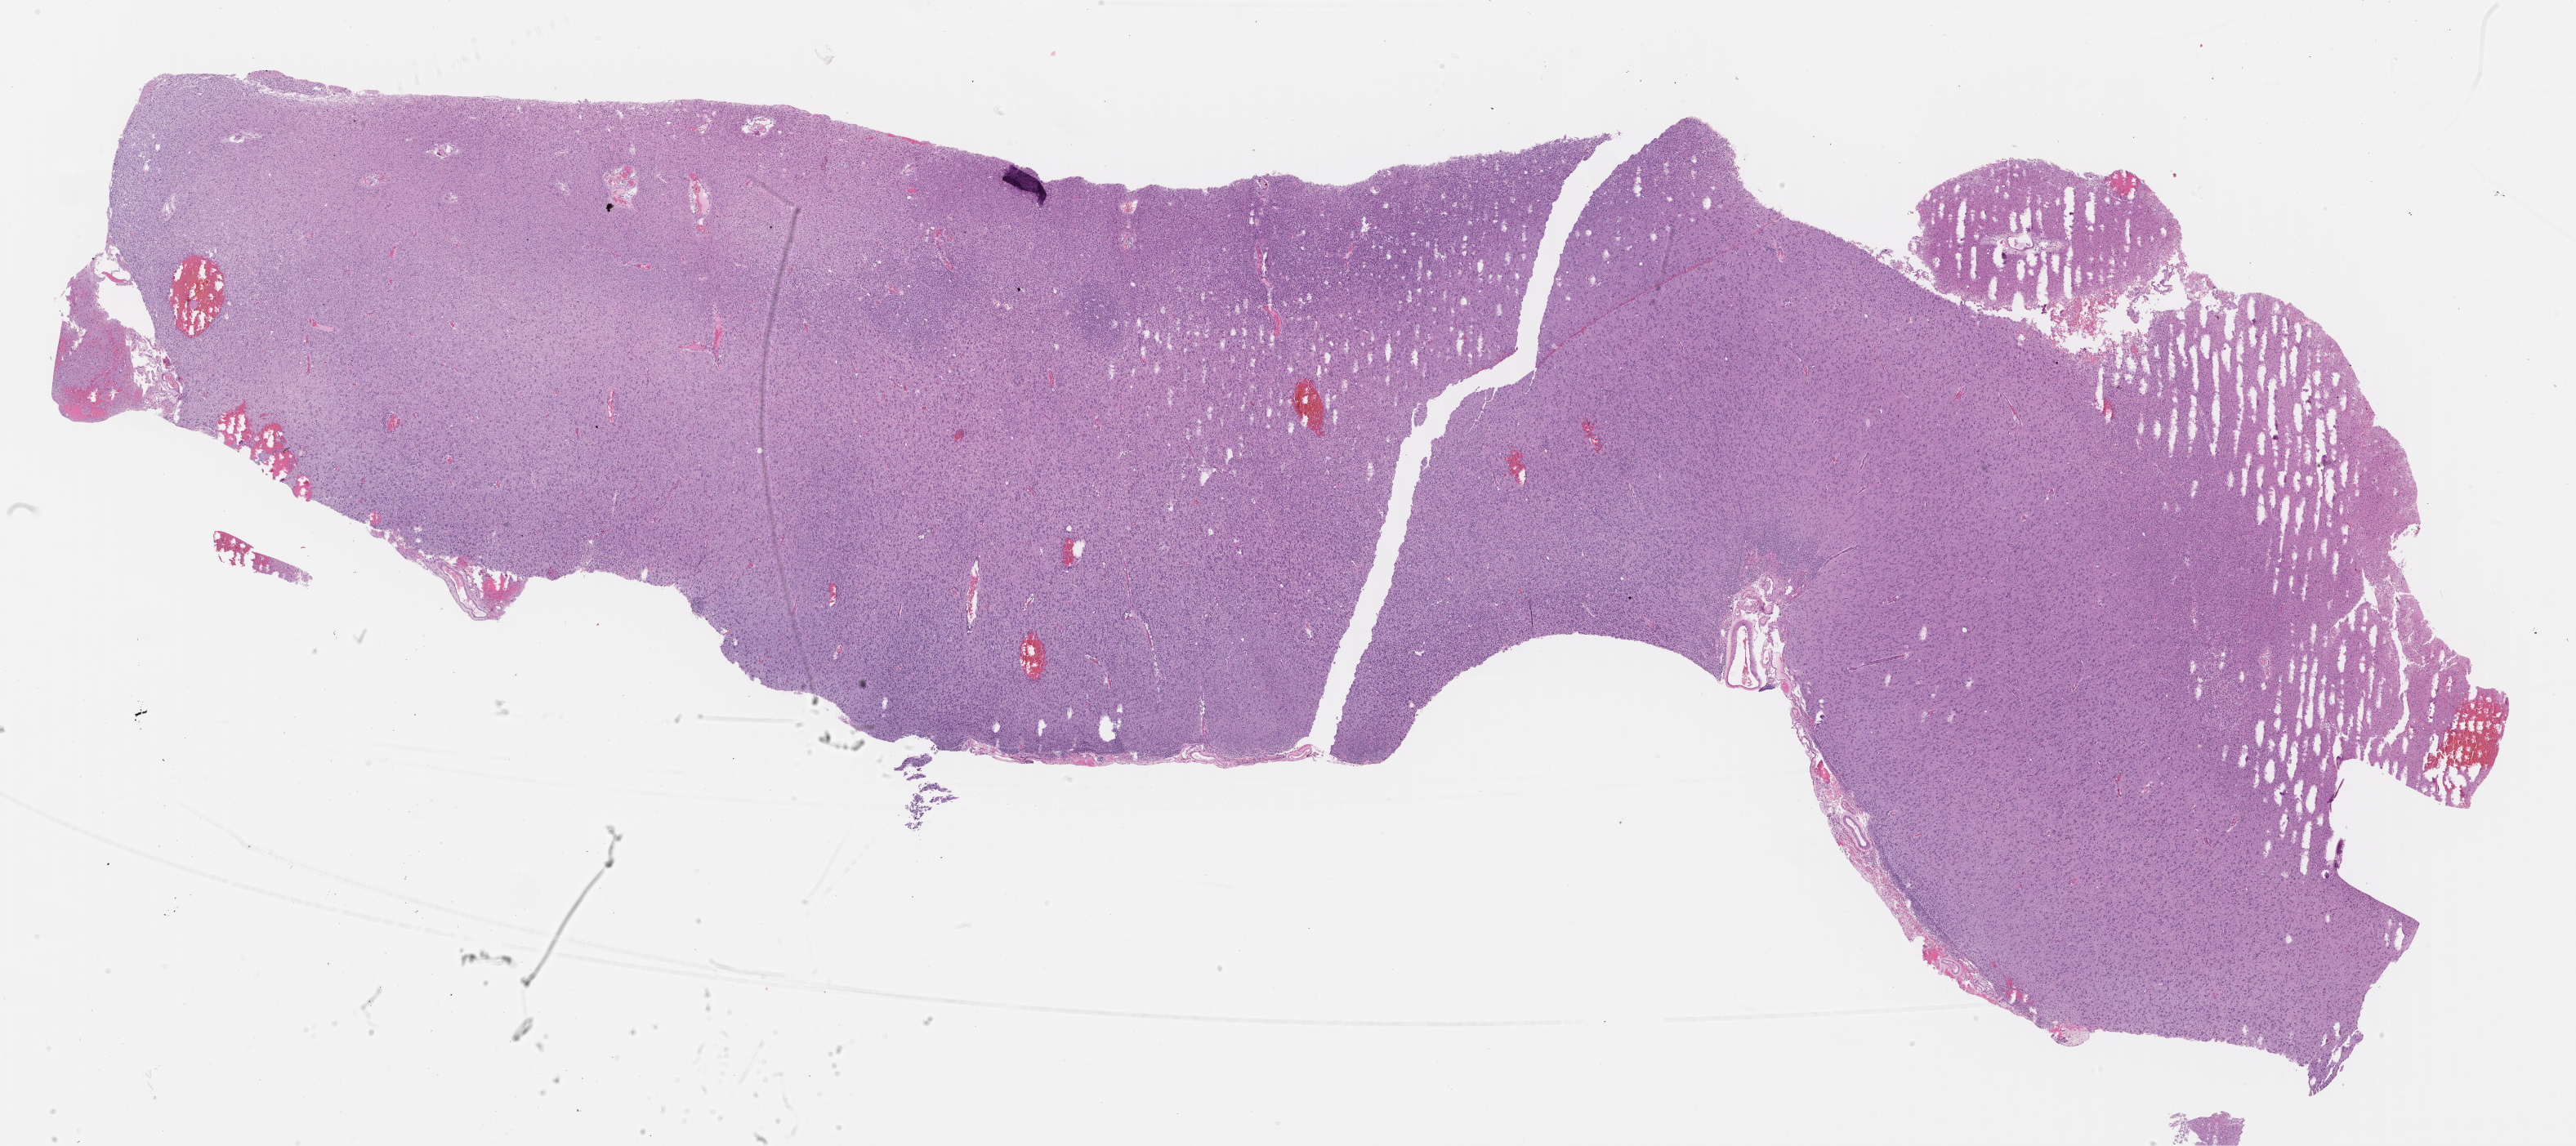
H&E whole-slide image — shown as a low-resolution overview of the whole scanned area (about 25.4 x 11.3 mm); FFPE section; sample: primary tumour, brain. Female, age 53 years at initial diagnosis. Histologic grade: G2 (moderately differentiated).
- laterality: right
- diagnosis: Oligodendroglioma, NOS (cerebrum)